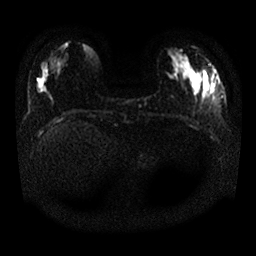
Breast MRI, one axial slice. Diffusion-weighted series; image 2 of 4 stored at this slice position (different b-values; order by instance number). 1.5 T. 4 mm slice thickness. 256 × 256 image matrix, field of view 340 × 340 mm. Female patient.
Annotated regions visible in this slice (expert manual segmentation):
- tumour on diffusion-weighted imaging: box from (x=202, y=77) to (x=216, y=99) px